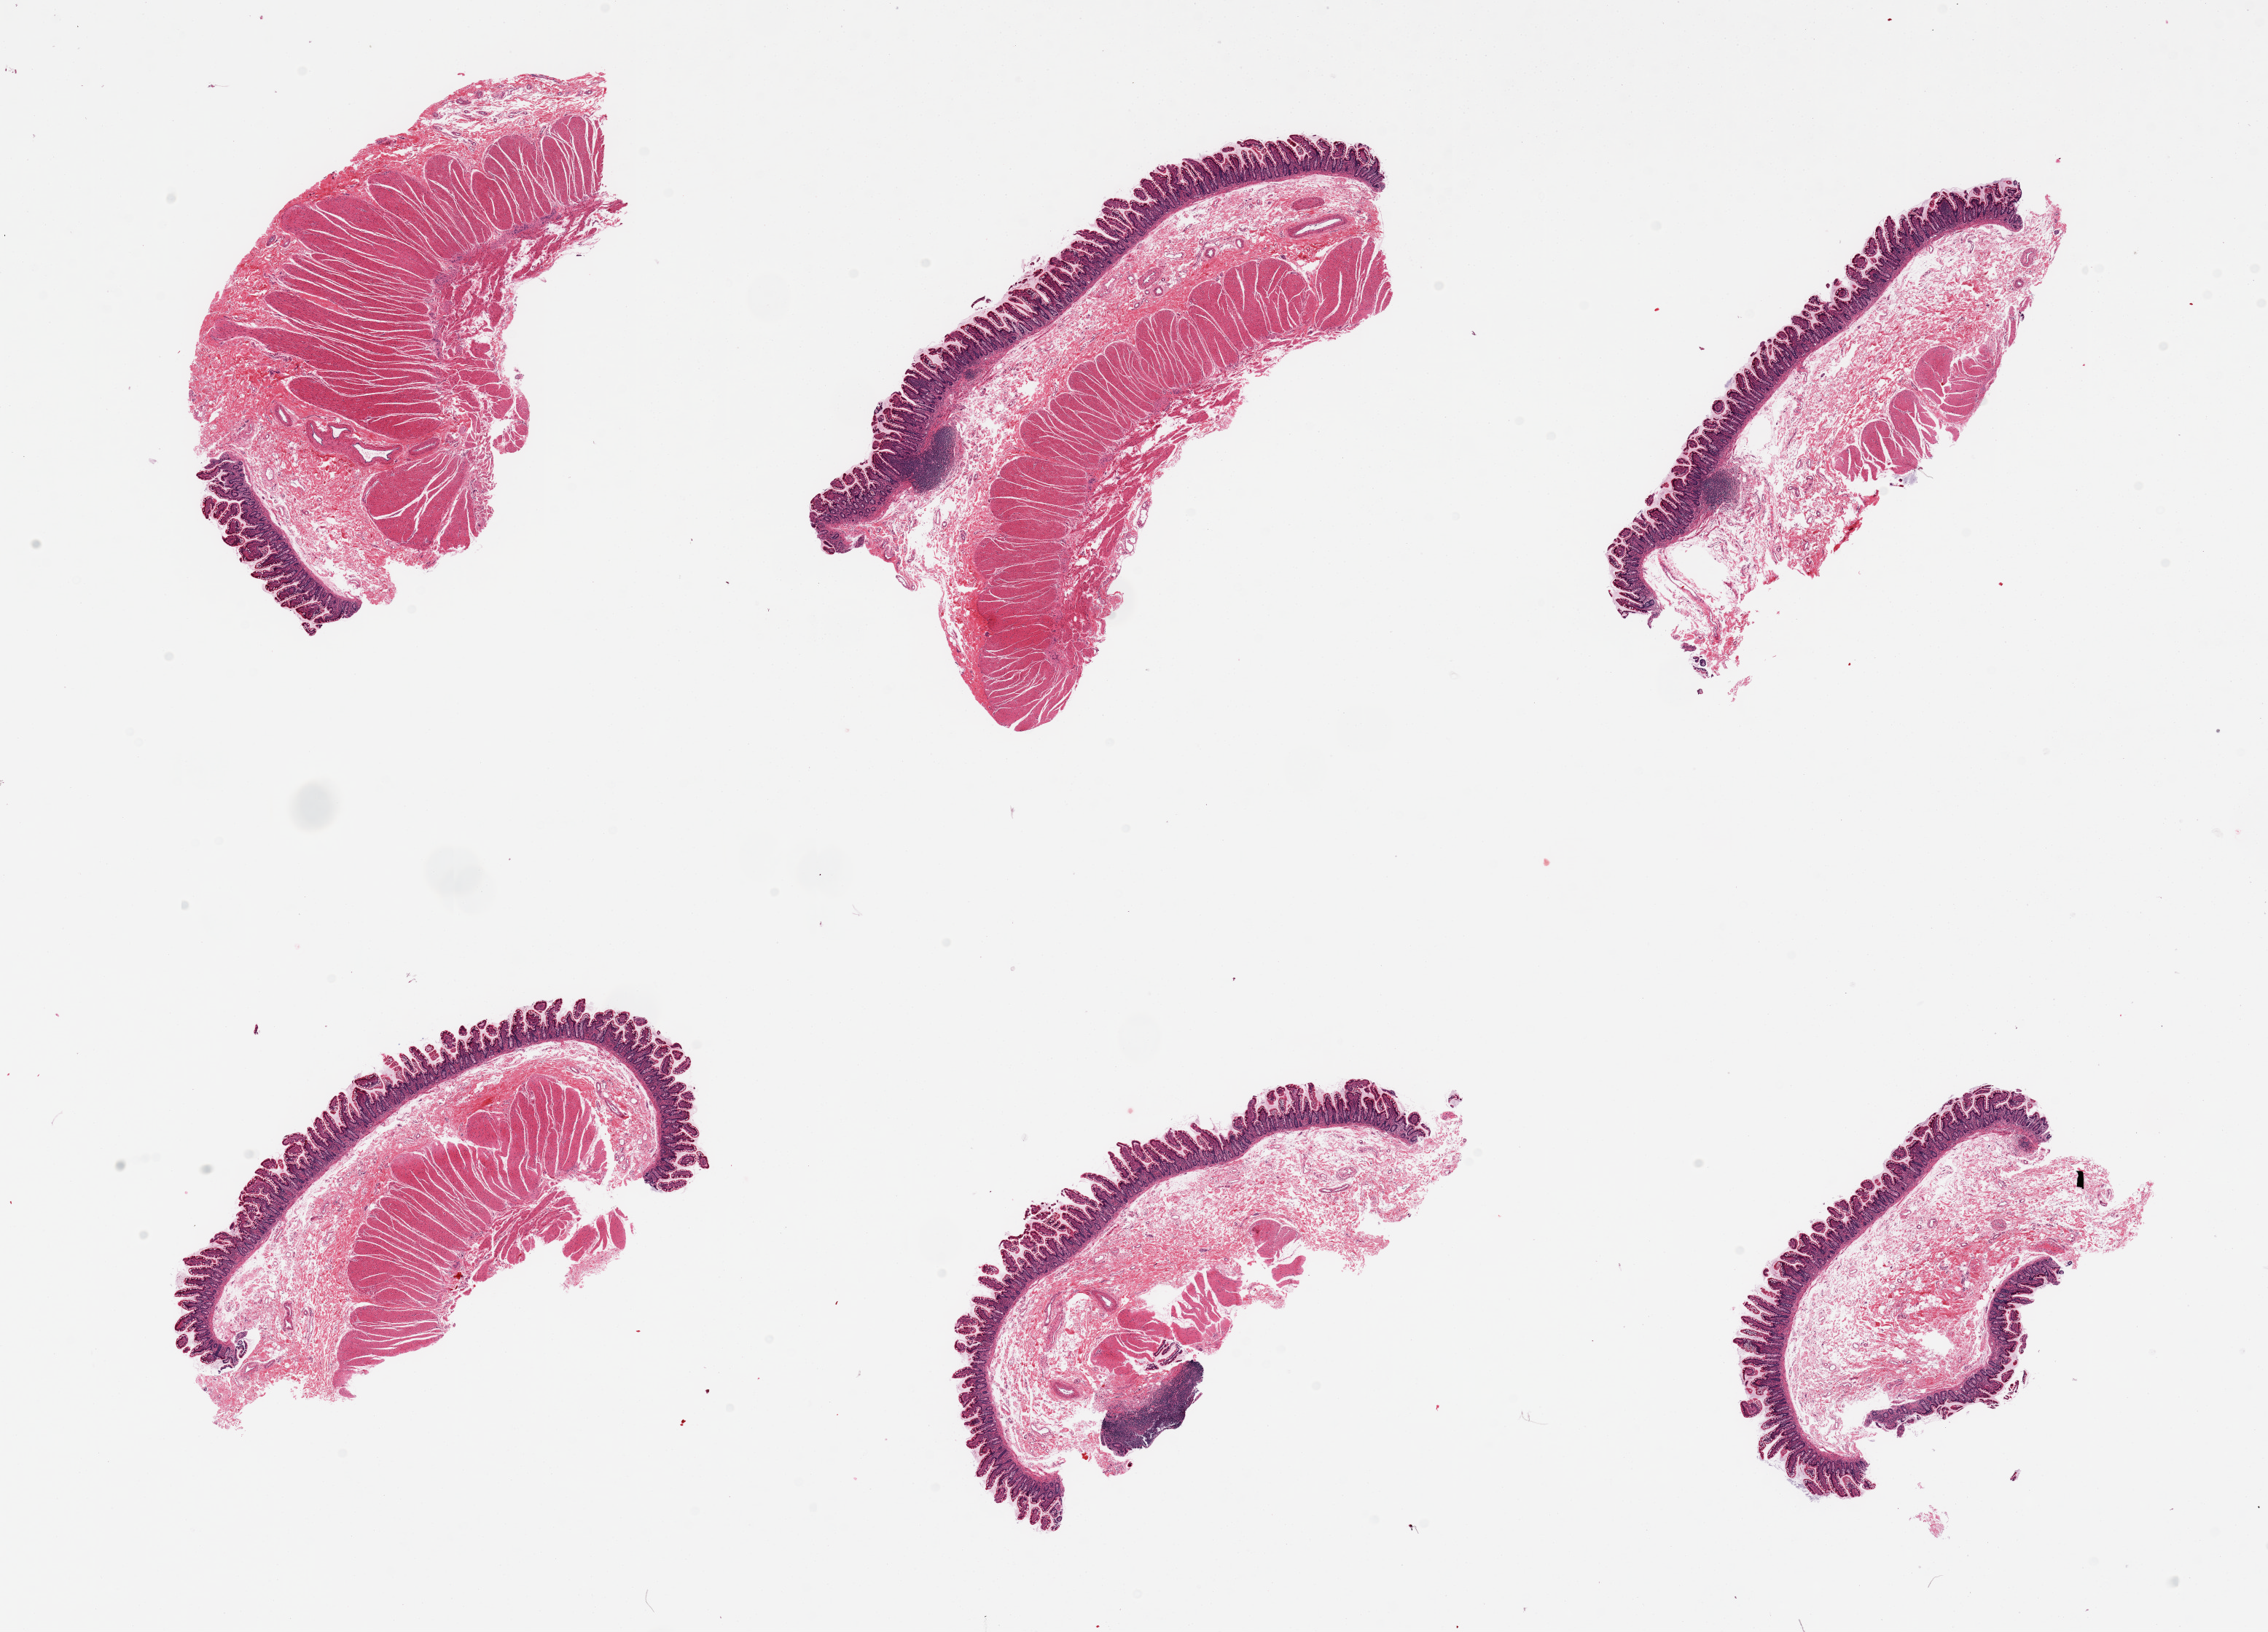
Digitized hematoxylin and eosin (H&E)-stained section, brightfield — low-resolution overview of the scanned area, about 24.6 x 17.7 mm (acquisition: 20x scan), PAXgene-fixed, paraffin-embedded tissue, sampled site (target tissue): ileum, donor tissue sample.
- review note (as recorded): 6 pieces; muscularis in 5 of 6; 3 small lymphoid nodules